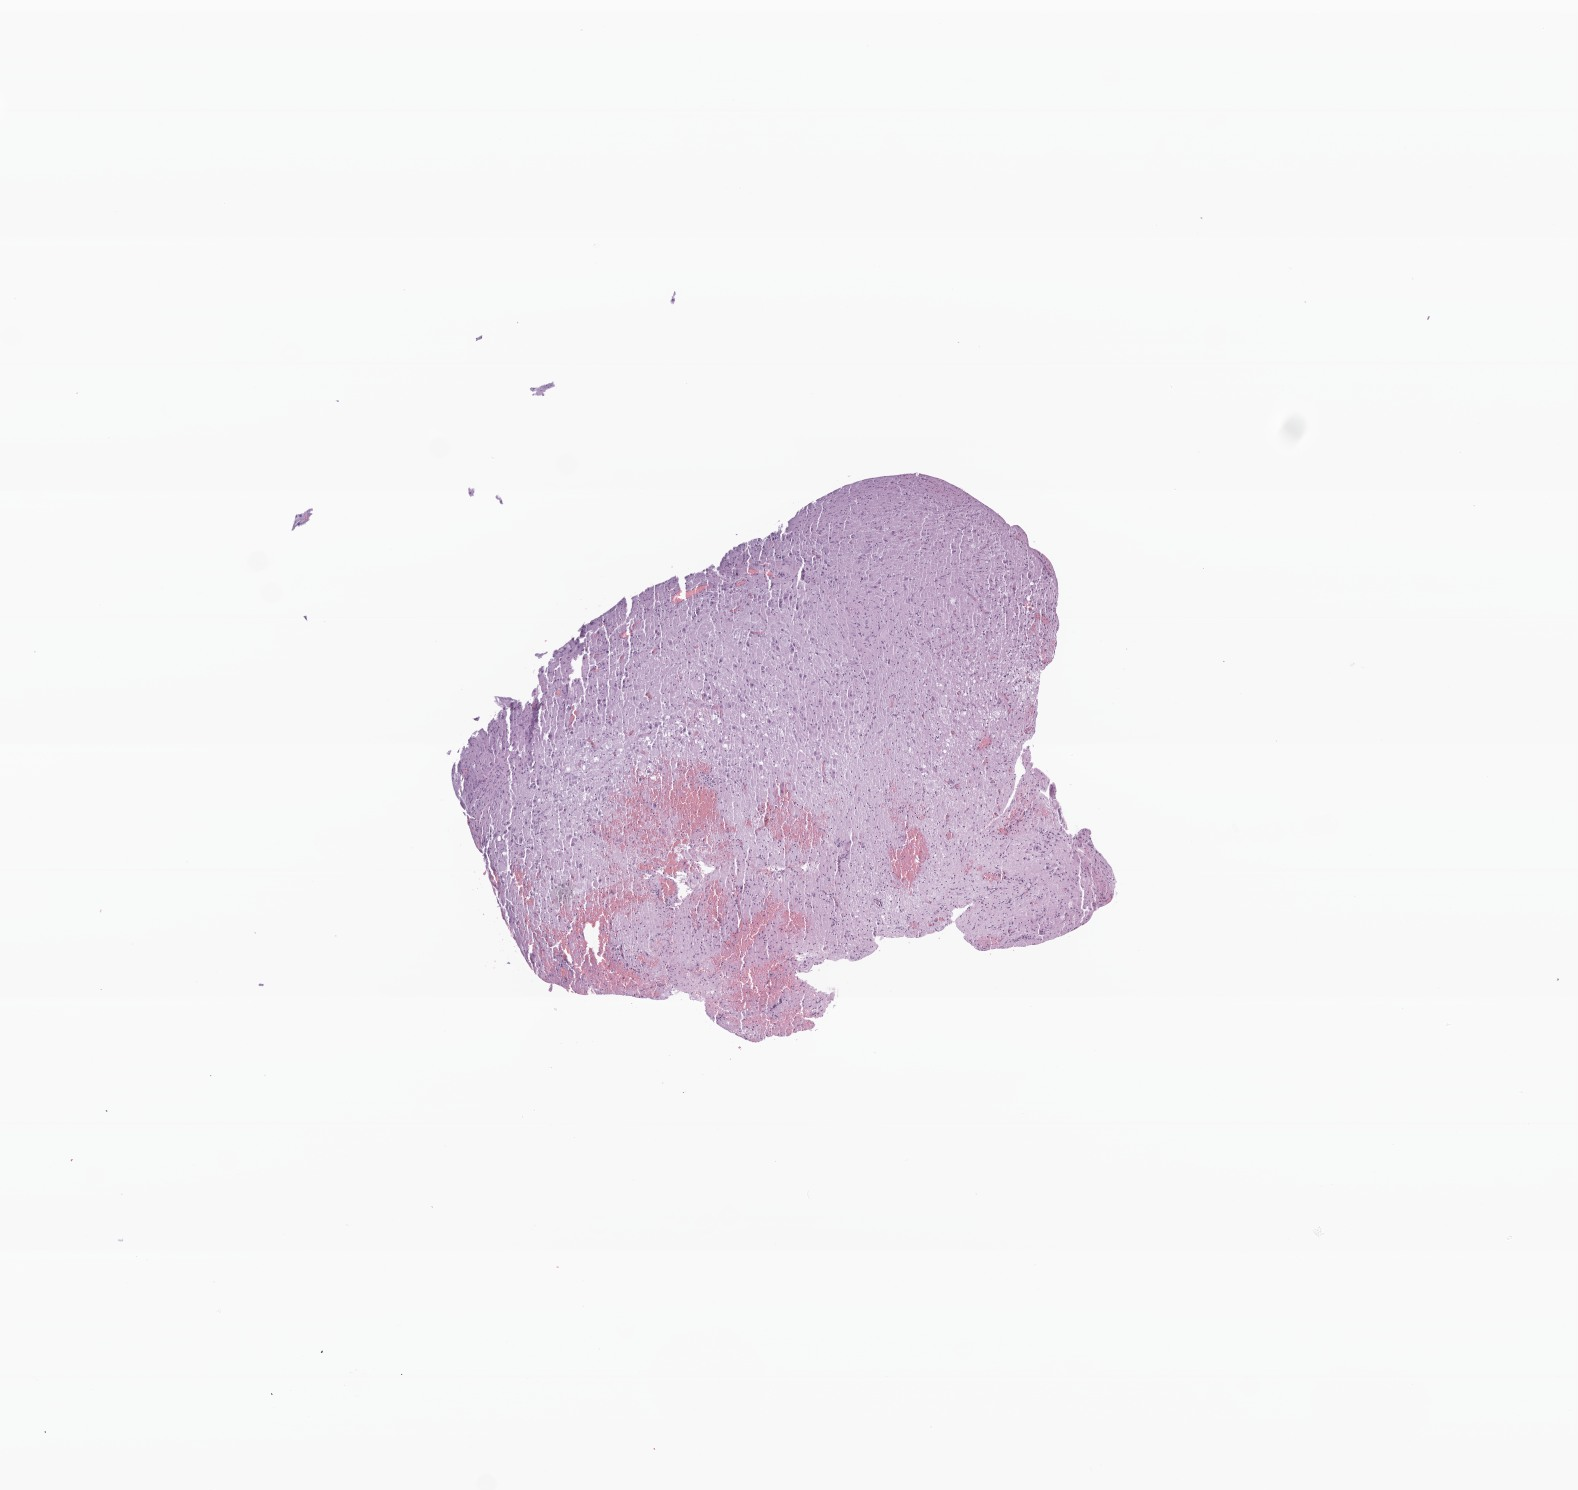
Haematoxylin and eosin whole-slide image of tumor tissue from the brain — low-resolution overview of the scanned area, about 6.6 x 6.3 mm, formalin-fixed, paraffin-embedded (FFPE) tissue. Female patient, age 91 months.
Diagnosis: Ganglioglioma, NOS.